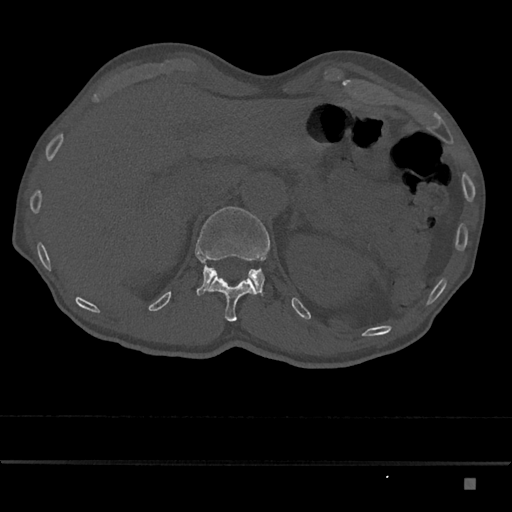
CT including the spine, one axial slice; slice 581 of 797 in the series (ordered by position); 120 kVp; bone window (W 1800 / L 400 HU); 0.5 mm slice thickness; 512 × 512 image matrix. Male patient, age 72 years. From the clinical record (not read from this slice): primary cancer: prostate.
Outlined on this slice (semi-automatically segmented with operator editing):
- L1 vertebra: bounding box [x1, y1, x2, y2] px = [195, 207, 270, 296]
- T12 vertebra: [203, 275, 256, 322]